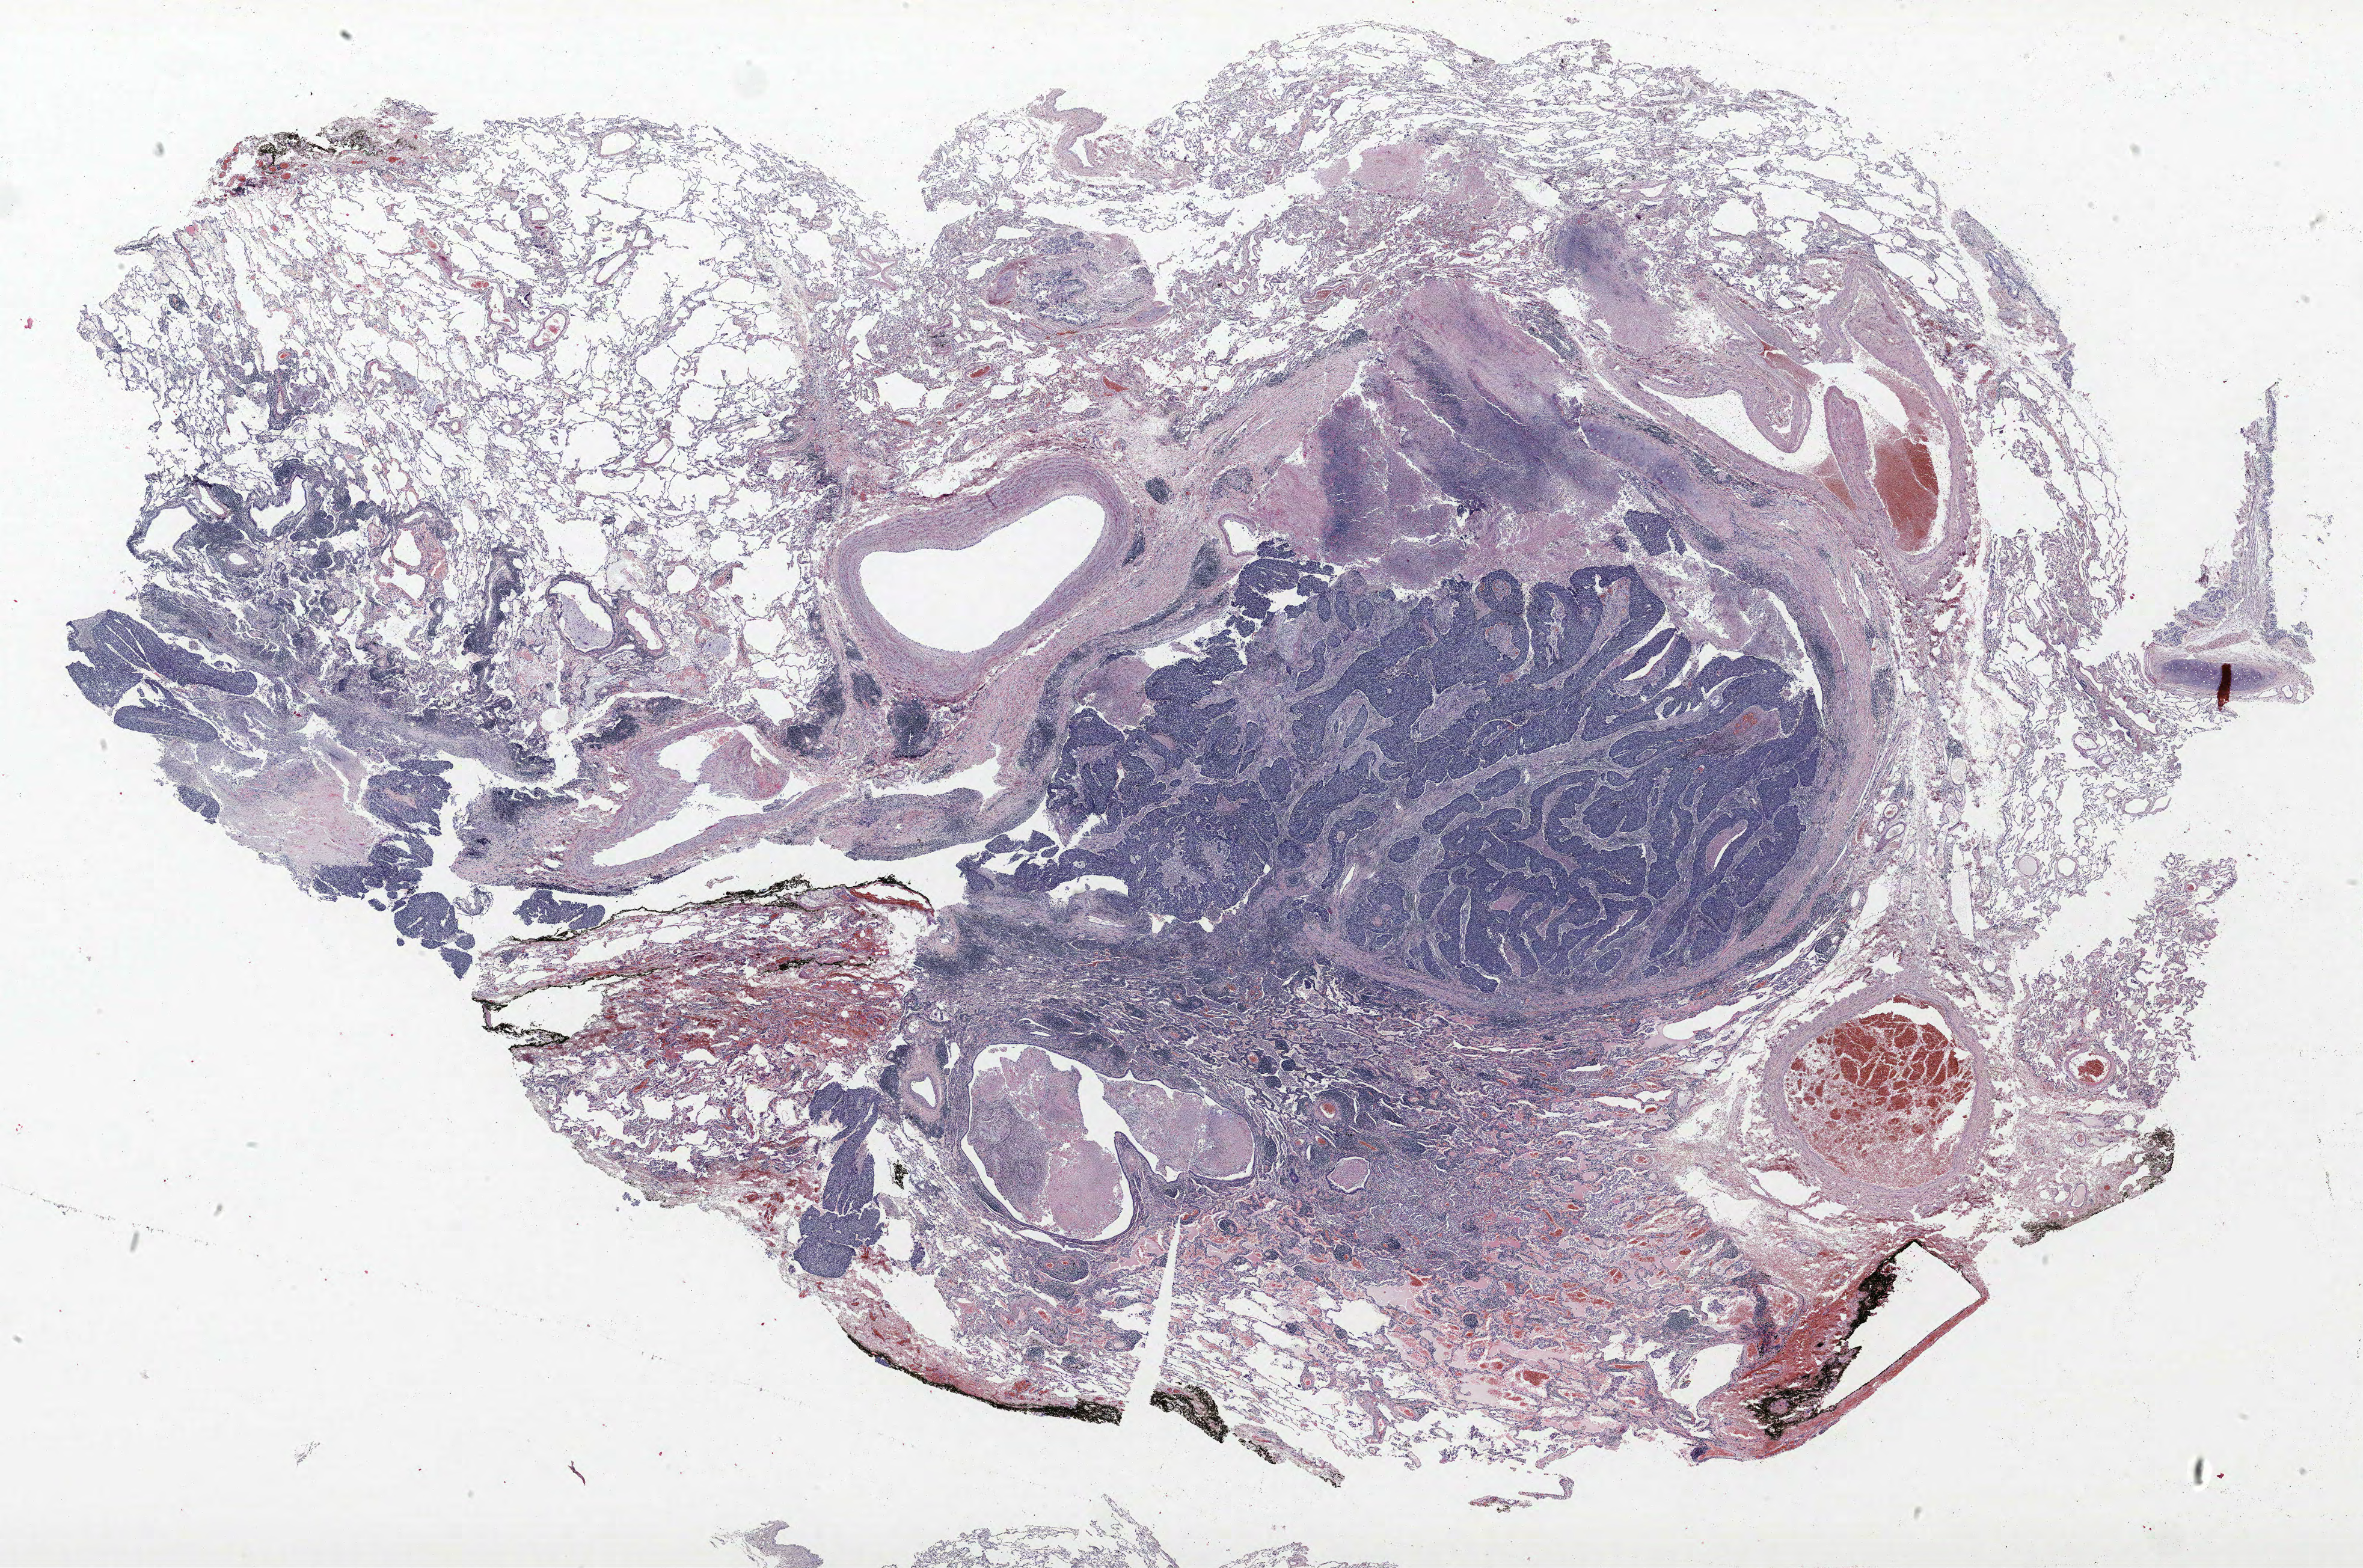
Whole-slide histology image, H&E-stained, whole scanned area (about 31.4 x 20.9 mm, acquisition: 40x scan) shown as a low-resolution overview. FFPE section. Lung. Male, age 66 at enrolment.
Primary tumour location (clinical record): left upper lobe. Stage (AJCC 6th edition): IA. ICD-O-3 topography: upper lobe of lung (C34.1). Participant's lung-cancer diagnosis: Squamous cell carcinoma, NOS. Tumour size (pathology): 23 mm. Note: participant had 2 primary lung cancers recorded; fields above describe the first.